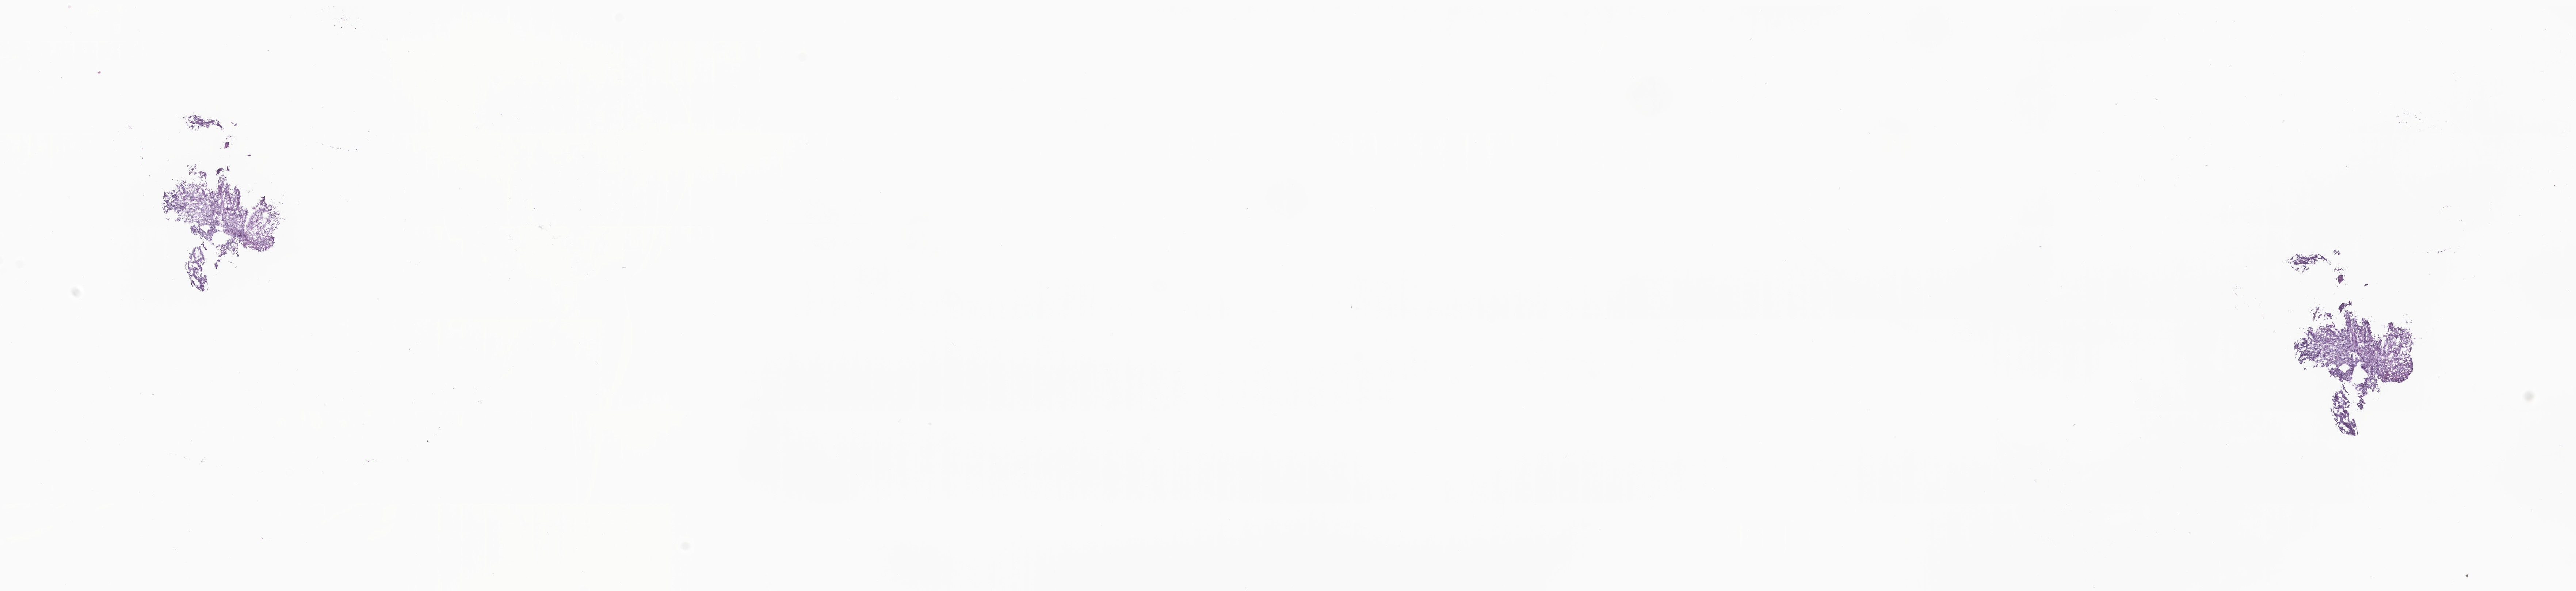
H&E whole-slide image, shown as a low-resolution overview of the whole scanned area (about 29.7 x 6.8 mm), cryosection, primary tumor, anatomic site: endometrium. Patient sex: female. Slide review estimates, as recorded: tumor cells 90%, tumor nuclei 90%, stromal cells 10%, necrosis 0%, normal cells 0%. Inflammatory infiltration, as recorded: lymphocyte infiltration 2%, monocyte infiltration 2%, neutrophil infiltration 3%.
Section: bottom of the tissue portion. AJCC pathologic stage: Stage IIIC2. Diagnosis: Serous carcinoma, NOS.